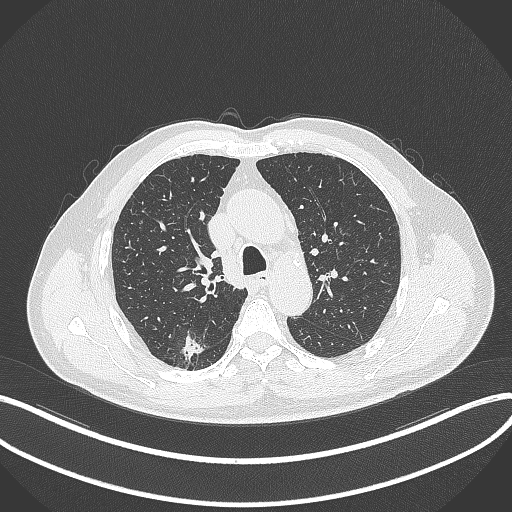
Chest CT, one axial slice; slice 259 of 359 in the series (ordered by position); lung window (W 1500 / L -600 HU); 512 × 512 image matrix, field of view 400 × 400 mm. Patient: male, 69 years. Case-level facts recorded for this patient, not image findings: clinical TNM (as recorded): T1b N0 M0.
Outlined on this slice (bounding box drawn by a radiologist):
- lung tumour (recorded histology: adenocarcinoma): bounding box <179,330,208,364> (left, top, right, bottom; pixels)